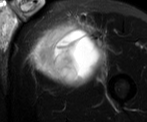
MRI of an extremity soft-tissue mass, one axial slice. Position 44 of 52 along the scan axis. T2-weighted fat-saturated. MR volume resampled by the dataset authors to the PET/CT grid (not the native acquisition matrix). 3.27 mm slice thickness. 147 × 122 image matrix, field of view 144 × 119 mm. Male patient. Case-level facts recorded for this patient, not image findings: histological type: pleiomorphic liposarcoma; grade: high; site of the primary tumour: left thigh.
Outlined on this slice (expert contour drawn on MRI and transferred to this co-registered scan by the dataset authors):
- gross tumour volume including surrounding oedema: bounding box <37,21,104,77> (left, top, right, bottom; pixels)
- gross tumour volume (mass): <37,28,95,77>